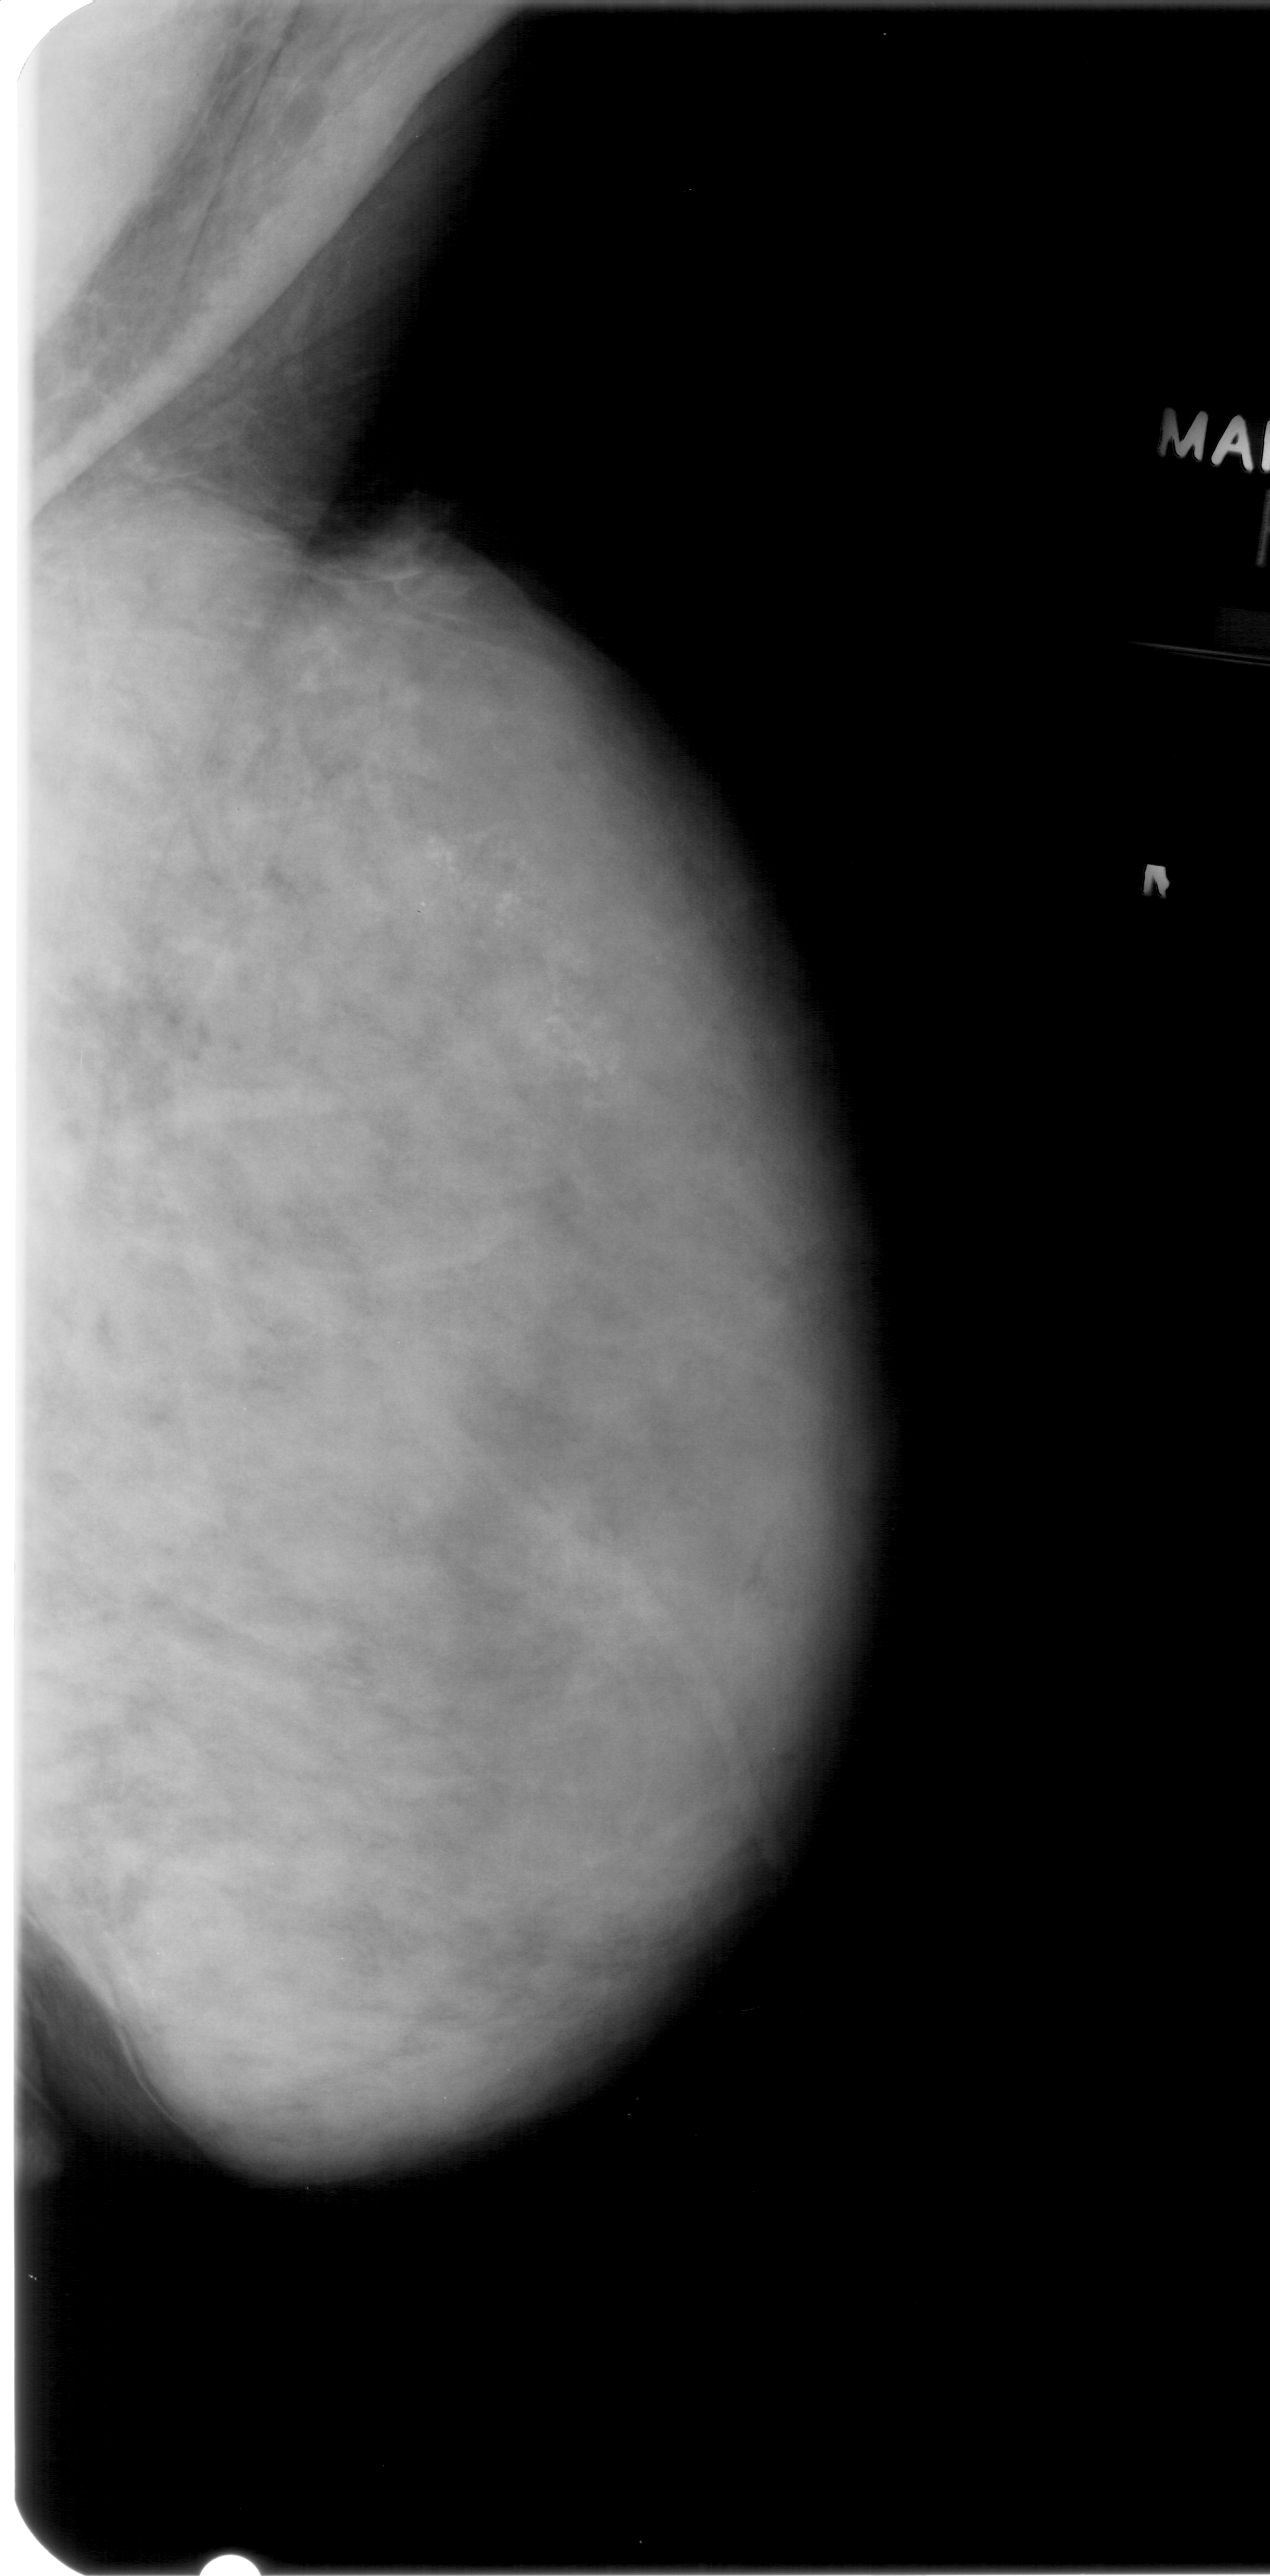
Scanned film-screen mammogram. Right breast. MLO view. 1270 × 2576 image matrix.
Expert-marked regions of interest on this film, with their recorded descriptors:
- calcifications, morphology amorphous, distribution segmental; BI-RADS assessment category 4; subtlety rating 3 on a 1 (subtle) to 5 (obvious) scale; pathology (as recorded): benign: box from (x=378, y=789) to (x=691, y=1106) px